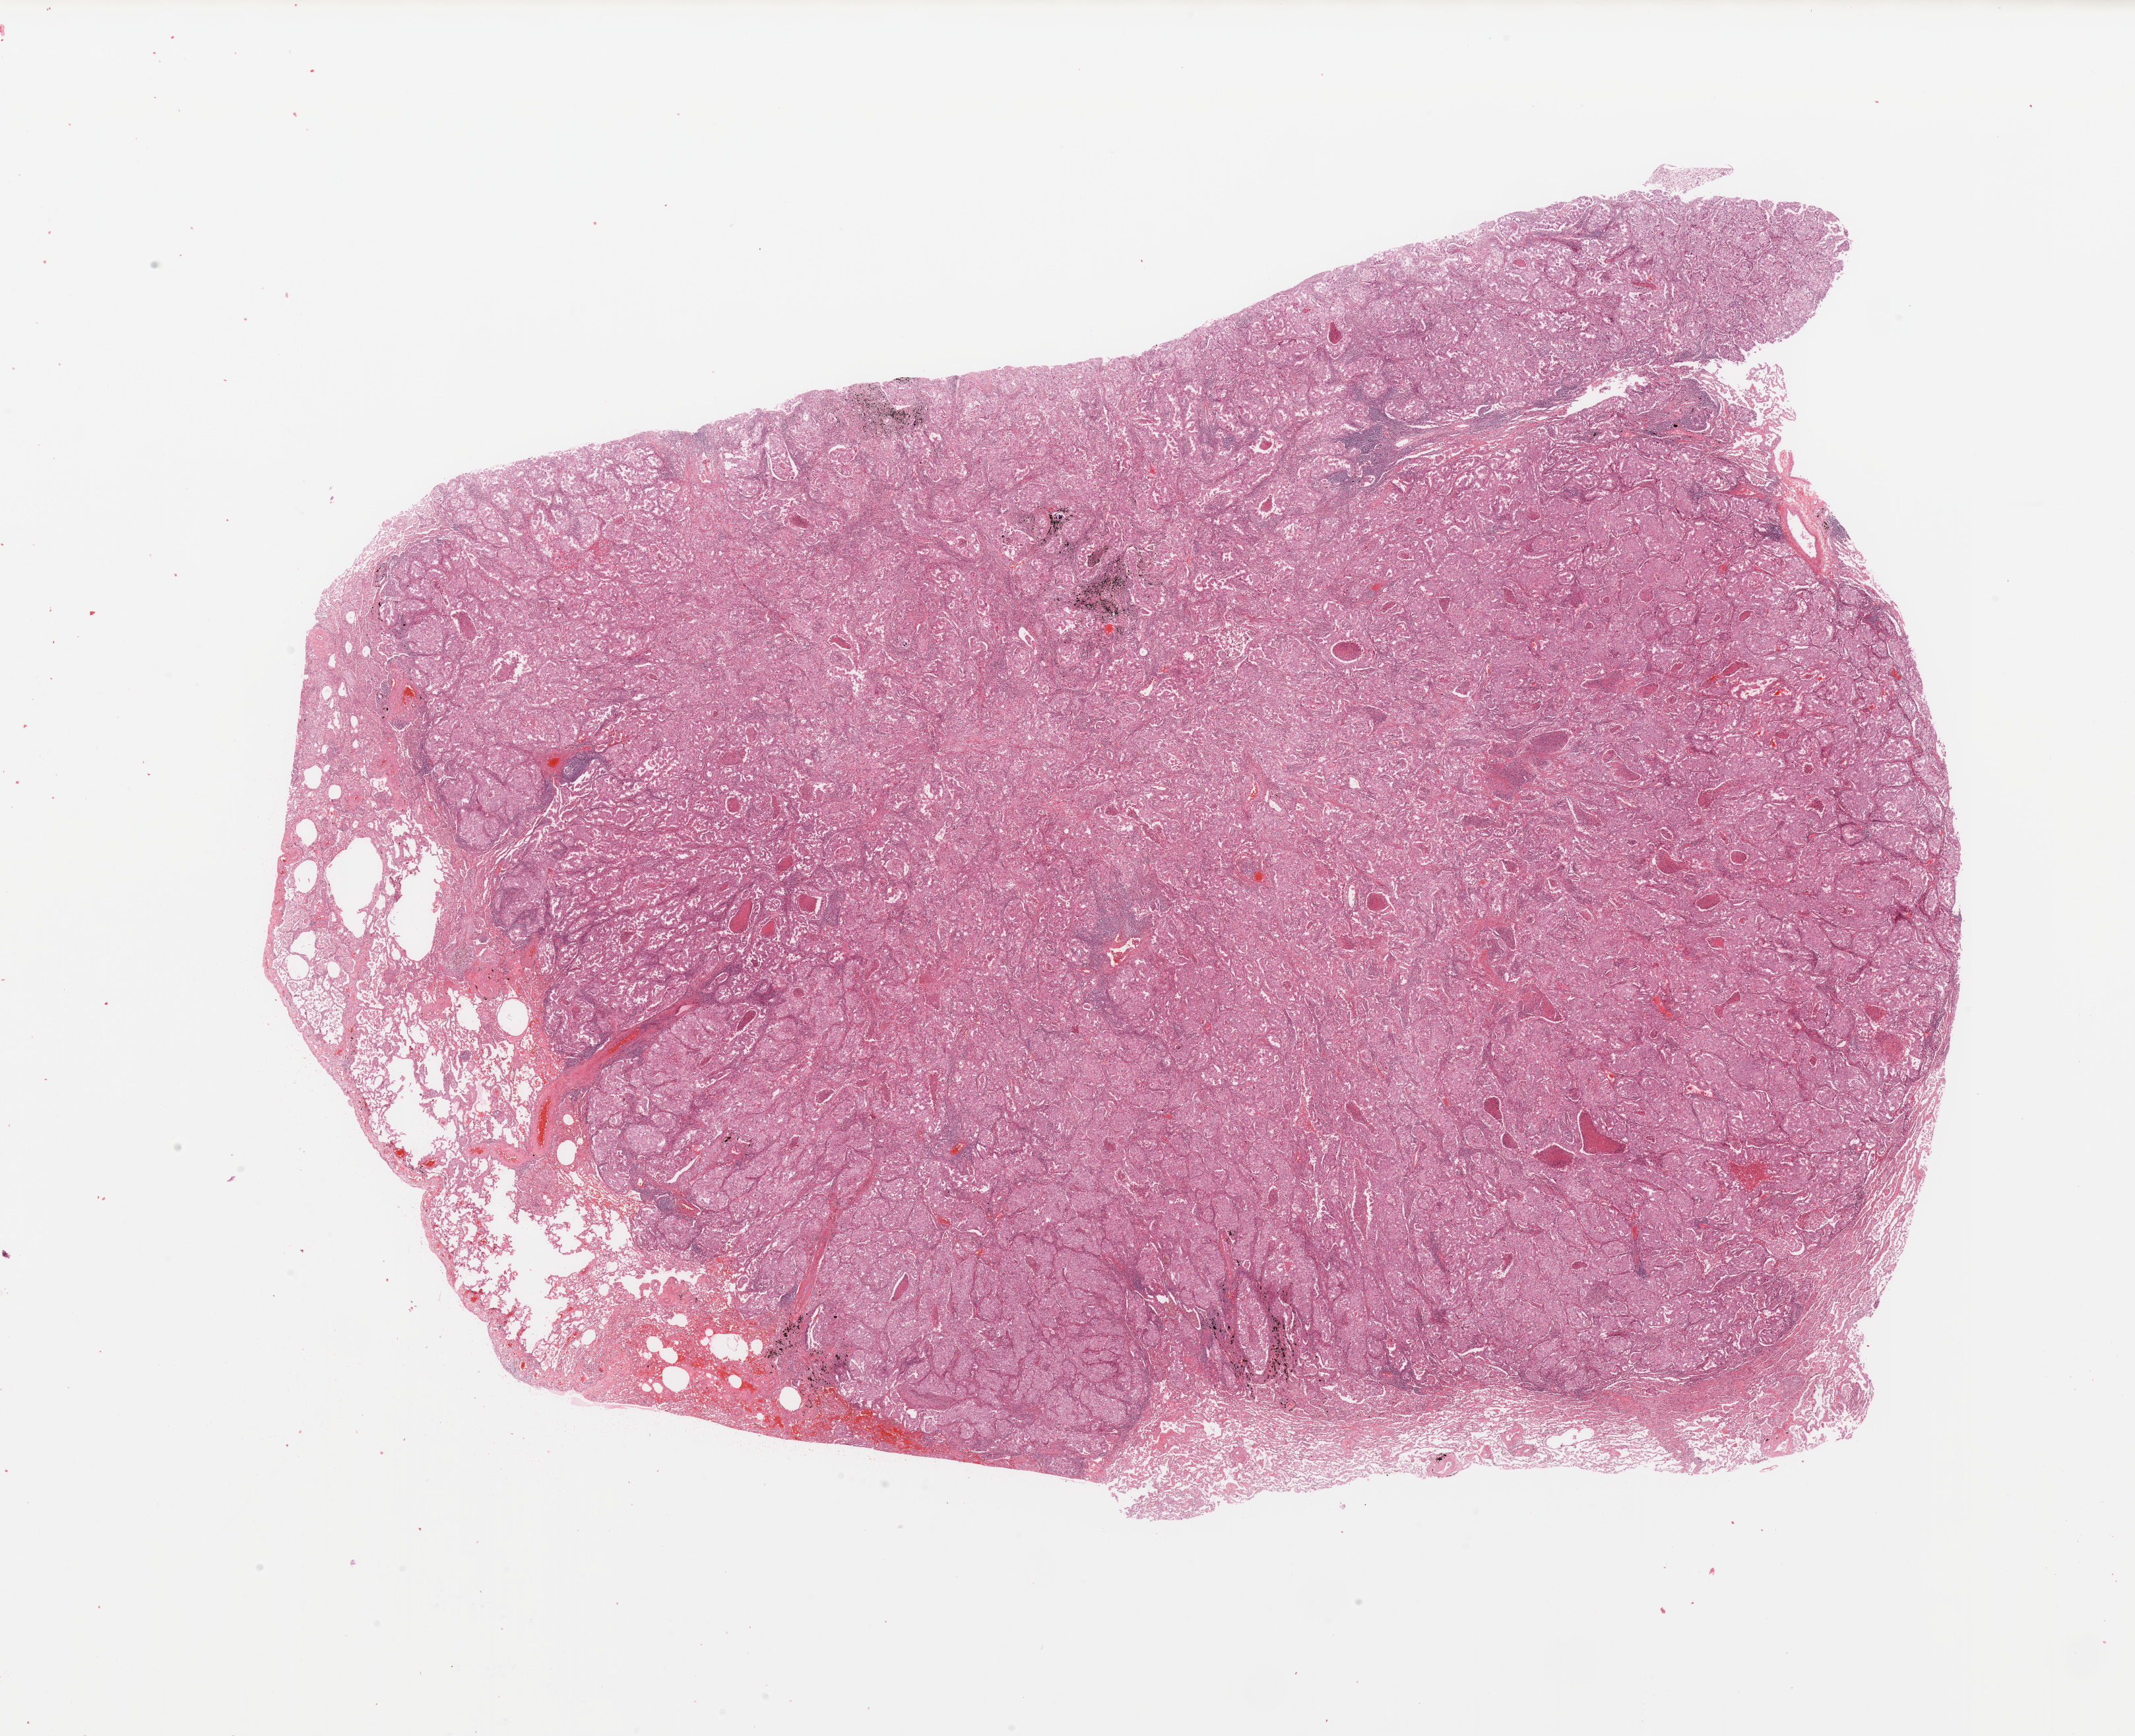
Digitized H&E-stained tissue section (whole slide), low-resolution overview of the scanned area, about 25.6 x 20.8 mm (acquisition: 20x scan); tumour tissue sample, sampled site: lung. Patient: male, age 56 years.
Diagnosis: Adenocarcinoma, NOS.